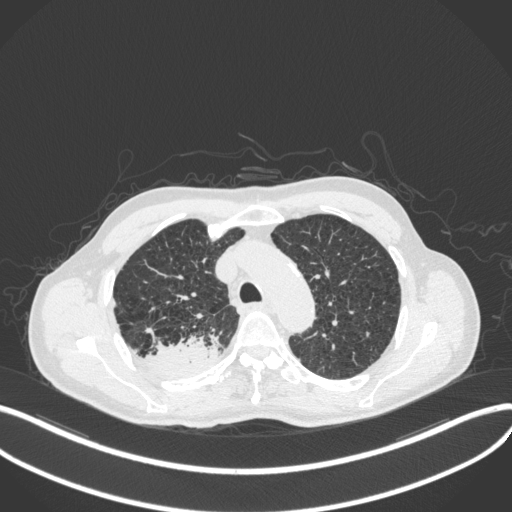
Chest CT, one axial slice; position 334 of 423 along the scan axis; reconstruction kernel B31f; 120 kVp; lung window (W 1500 / L -600 HU); 1 mm slice thickness; 512 × 512 image matrix, field of view 400 × 400 mm. Patient: male, 79 years. Case-level facts recorded for this patient, not image findings: clinical TNM (as recorded): T3 N0 M0.
Outlined on this slice (bounding box drawn by a radiologist):
- lung tumour (recorded histology: adenocarcinoma): bounding box (x1, y1, x2, y2) in pixels: (140, 329, 222, 376)